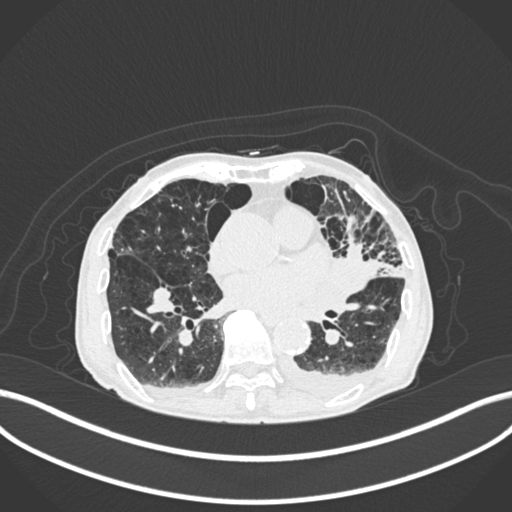
Chest CT, one axial slice. Slice 90 of 400 in the series (ordered by position). Reconstruction kernel B30f. Lung window (W 1500 / L -600 HU). 1 mm slice thickness. 512 × 512 image matrix. Male patient, age 90 years or older. Case-level facts recorded for this patient, not image findings: clinical TNM (as recorded): T2b N1 M0.
Outlined on this slice (bounding box drawn by a radiologist):
- lung tumour (recorded histology: squamous cell carcinoma): bounding box (x1, y1, x2, y2) in pixels: (337, 243, 383, 300)